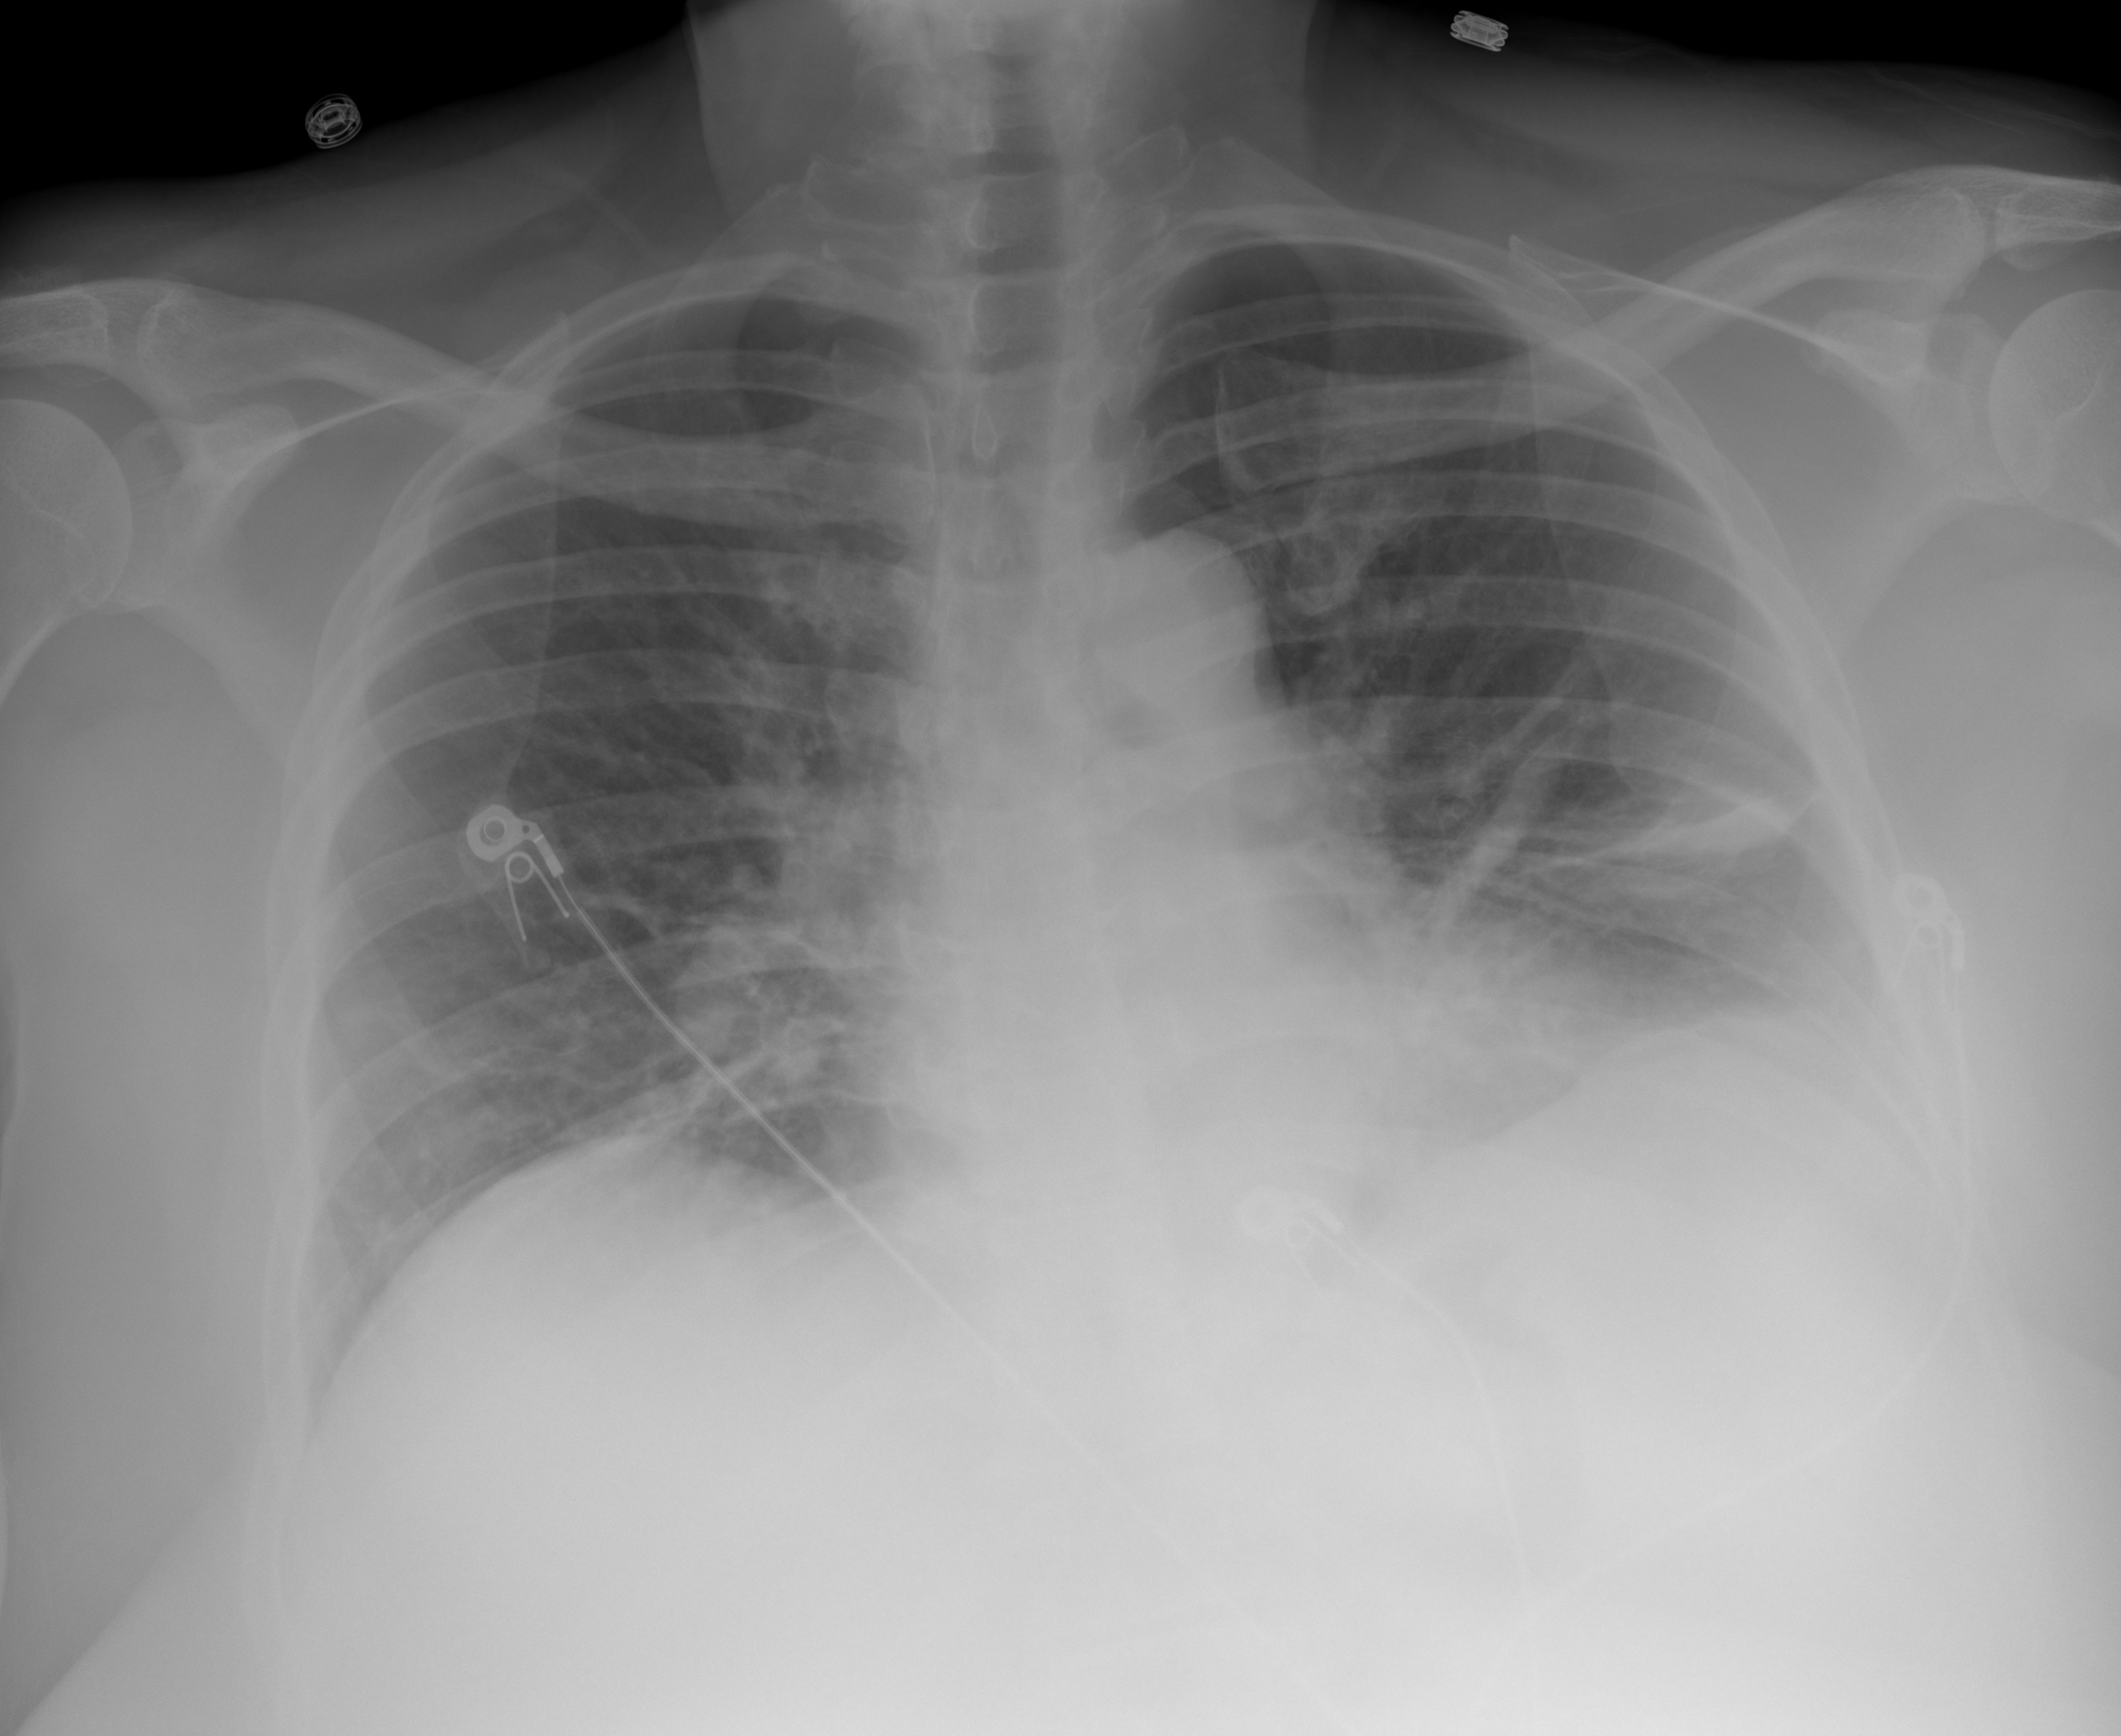
Portable chest radiograph, AP projection. Female patient, age 57 years; imaged 3 days after the COVID-19 diagnosis.
Radiologist's key findings for this exam: Patchy airspace opacity within the left lower lobe and to a lesser extent within the right lower lobe.